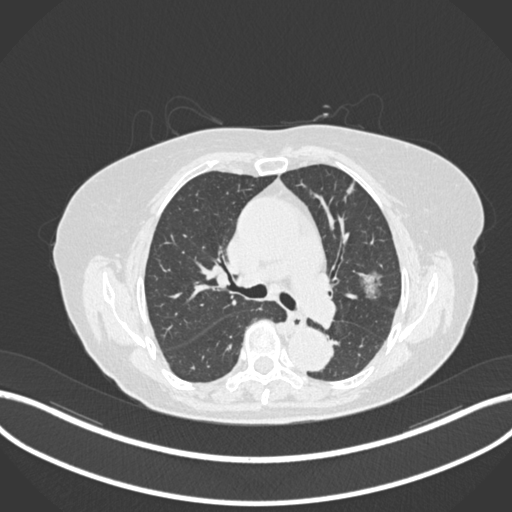
Chest CT, one axial slice. Slice 99 of 168 in the series (ordered by position). 120 kVp. Lung window (W 1500 / L -600 HU). 1 mm slice thickness. 512 × 512 image matrix. Female patient, age 75 years. From the clinical record (not read from this slice): clinical TNM (as recorded): T1c N0 M0.
Outlined on this slice (rectangle marked by the reading radiologist):
- lung tumour (recorded histology: adenocarcinoma): box from (x=353, y=266) to (x=385, y=300) px